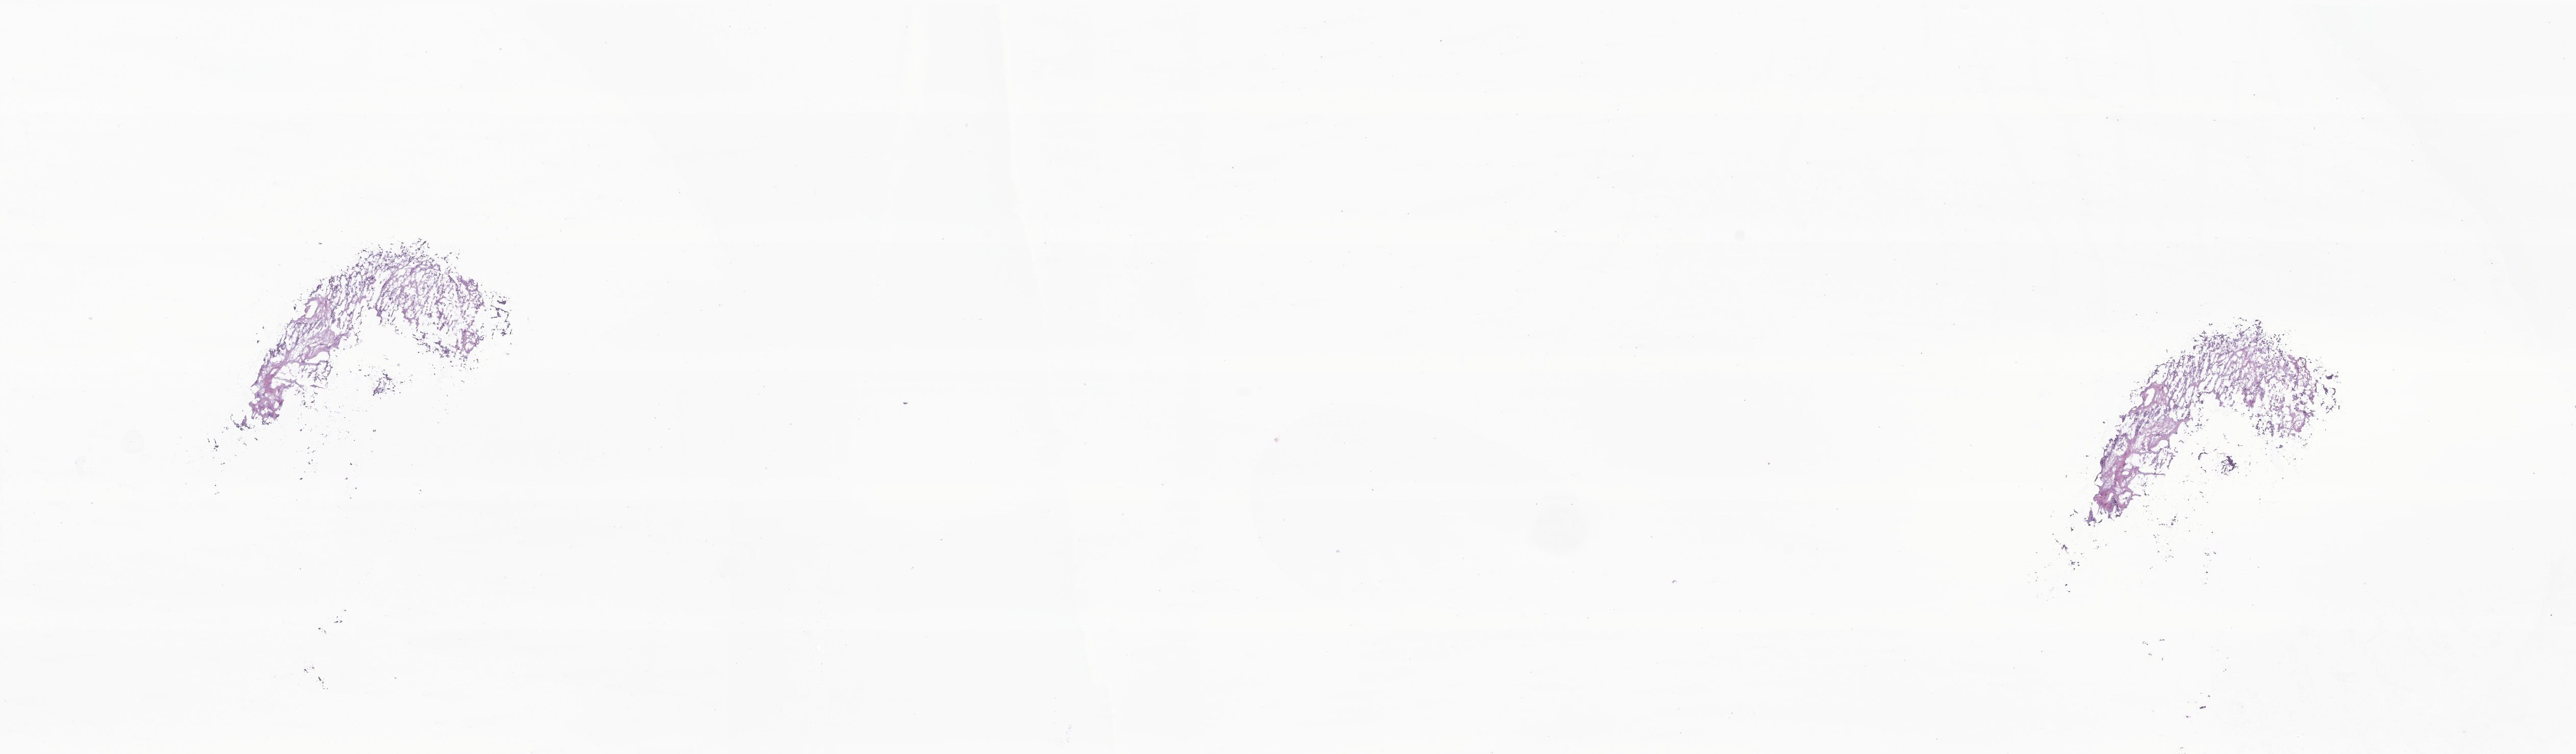
Whole-slide image, hematoxylin and eosin (H&E) stain of tumor tissue from the pelvis — low-resolution overview of the scanned area, about 21.3 x 6.2 mm, frozen section (OCT-embedded). Male patient, age 204 months (17 years).
Diagnosis (ICD-O-3 morphology term): Rhabdomyosarcoma, NOS.